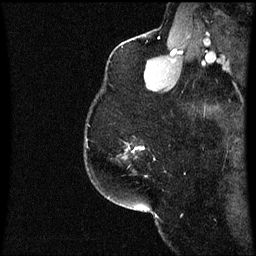
Breast MRI (dynamic contrast-enhanced), one sagittal slice; slice 50 of 60 in the series (ordered by position); dynamic contrast-enhanced series, image 2 of 3 at this slice position (ordered by acquisition); 1.5 T; TE 4.2 ms, TR 8.9 ms; 2 mm slice thickness; 256 × 256 image matrix, field of view 200 × 200 mm. Female patient, age 58 years. Case-level facts recorded for this patient, not image findings: setting: breast cancer imaged before/during neoadjuvant chemotherapy; receptor status: triple-negative.
Annotated regions visible in this slice (semi-automatic segmentation, software-assisted and operator-edited):
- analysis volume of interest (the breast-tissue region the enhancement analysis was run in; not a lesion): bounding box (x1, y1, x2, y2) in pixels: (124, 144, 157, 161)
- tumour enhancement mask (voxels above the 70 % enhancement threshold inside the analysis volume of interest): (136, 148, 145, 151)